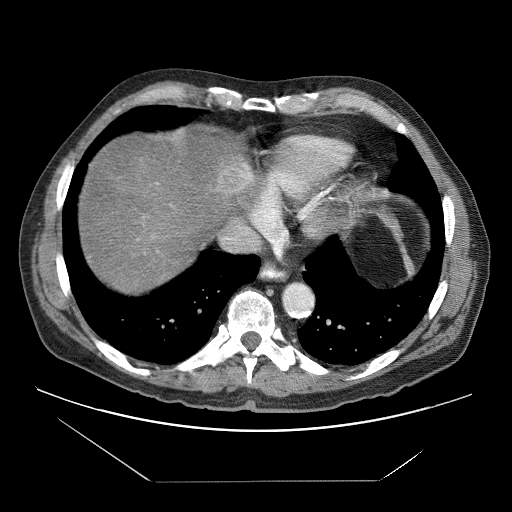
Contrast-enhanced abdominal CT (liver protocol), one axial slice. Position 67 of 83 along the scan axis. 120 kVp. Soft-tissue window (W 400 / L 40 HU). 2.5 mm slice thickness. 512 × 512 image matrix, field of view 420 × 420 mm. Case-level facts recorded for this patient, not image findings: diagnosis: hepatocellular carcinoma (patient treated with transarterial chemoembolisation; whether this scan precedes or follows treatment is not stated here); TNM stage (as recorded): Stage-IVB; Child-Pugh class: B; tumour differentiation: poorly differentiated; tumour nodularity: uninodular.
Outlined on this slice (semi-automatically segmented with operator editing):
- liver parenchyma outside the tumour (the mass and vessels are separate outlines, so this box may not span the whole liver): bounding box <78,134,248,292> (left, top, right, bottom; pixels)
- mass: <216,155,252,196>
- liver vessels: <137,183,158,240>